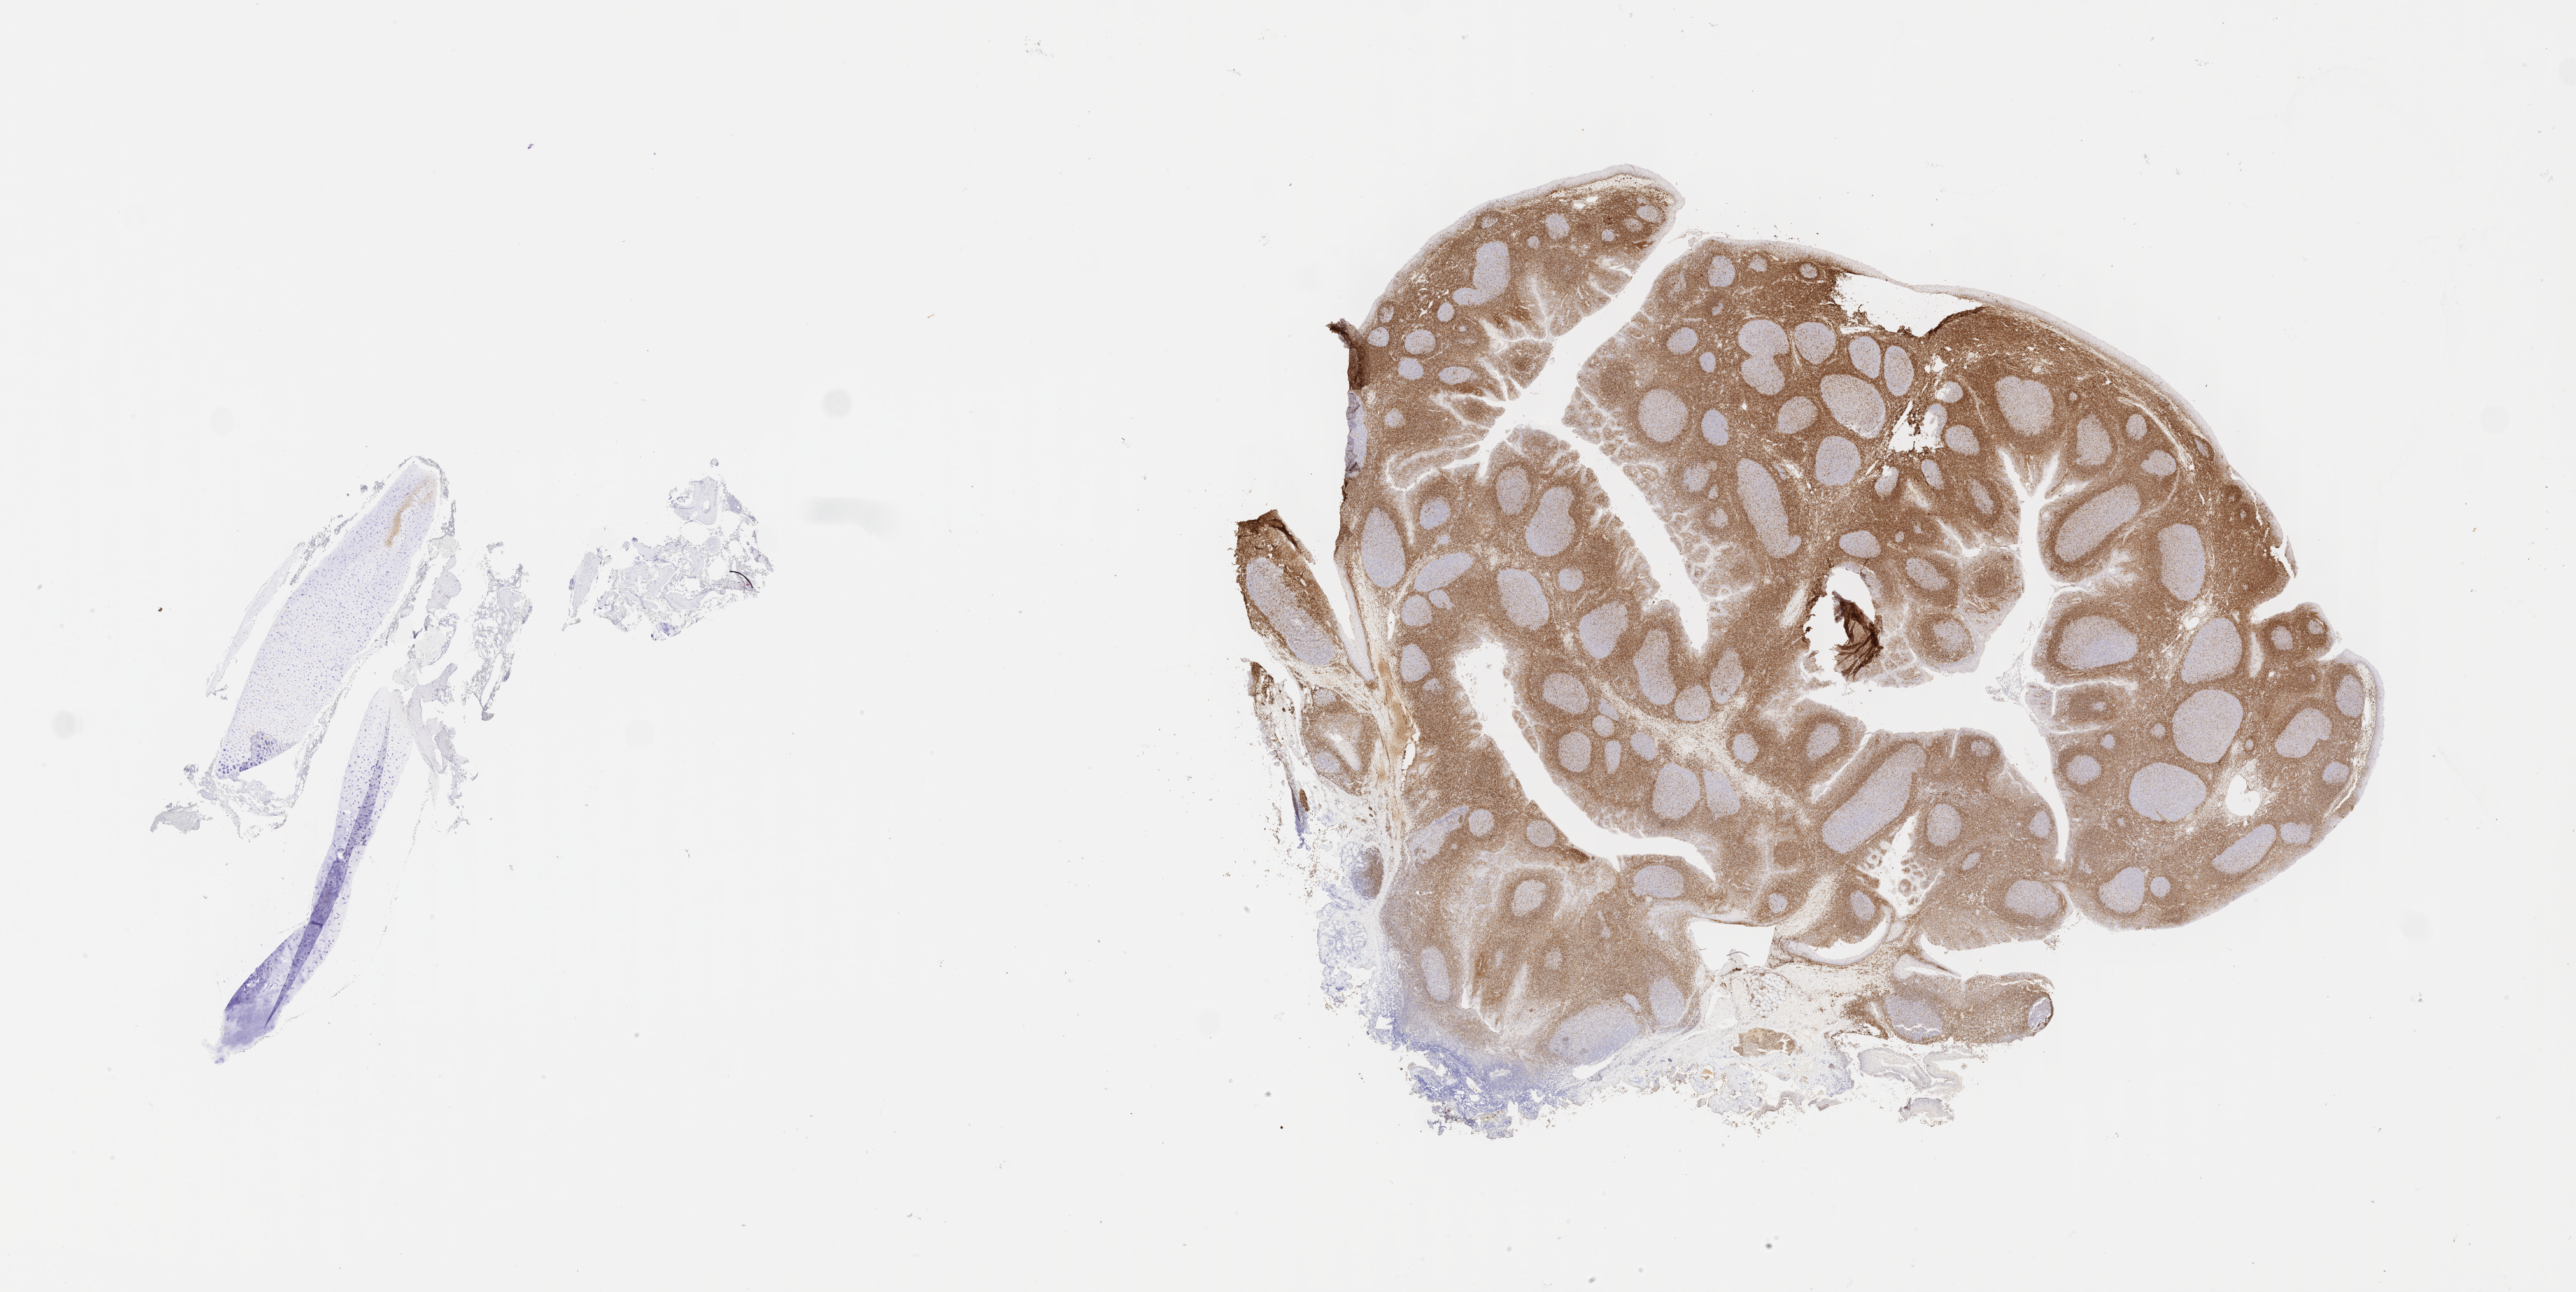
Whole-slide image, immunohistochemical stain for BCL2 — low-resolution overview of the scanned area, about 32.7 x 16.4 mm, specimen: tumor tissue, anatomic site: bone marrow. Female patient, age 11 years.
Histologic diagnosis: Burkitt lymphoma, NOS.